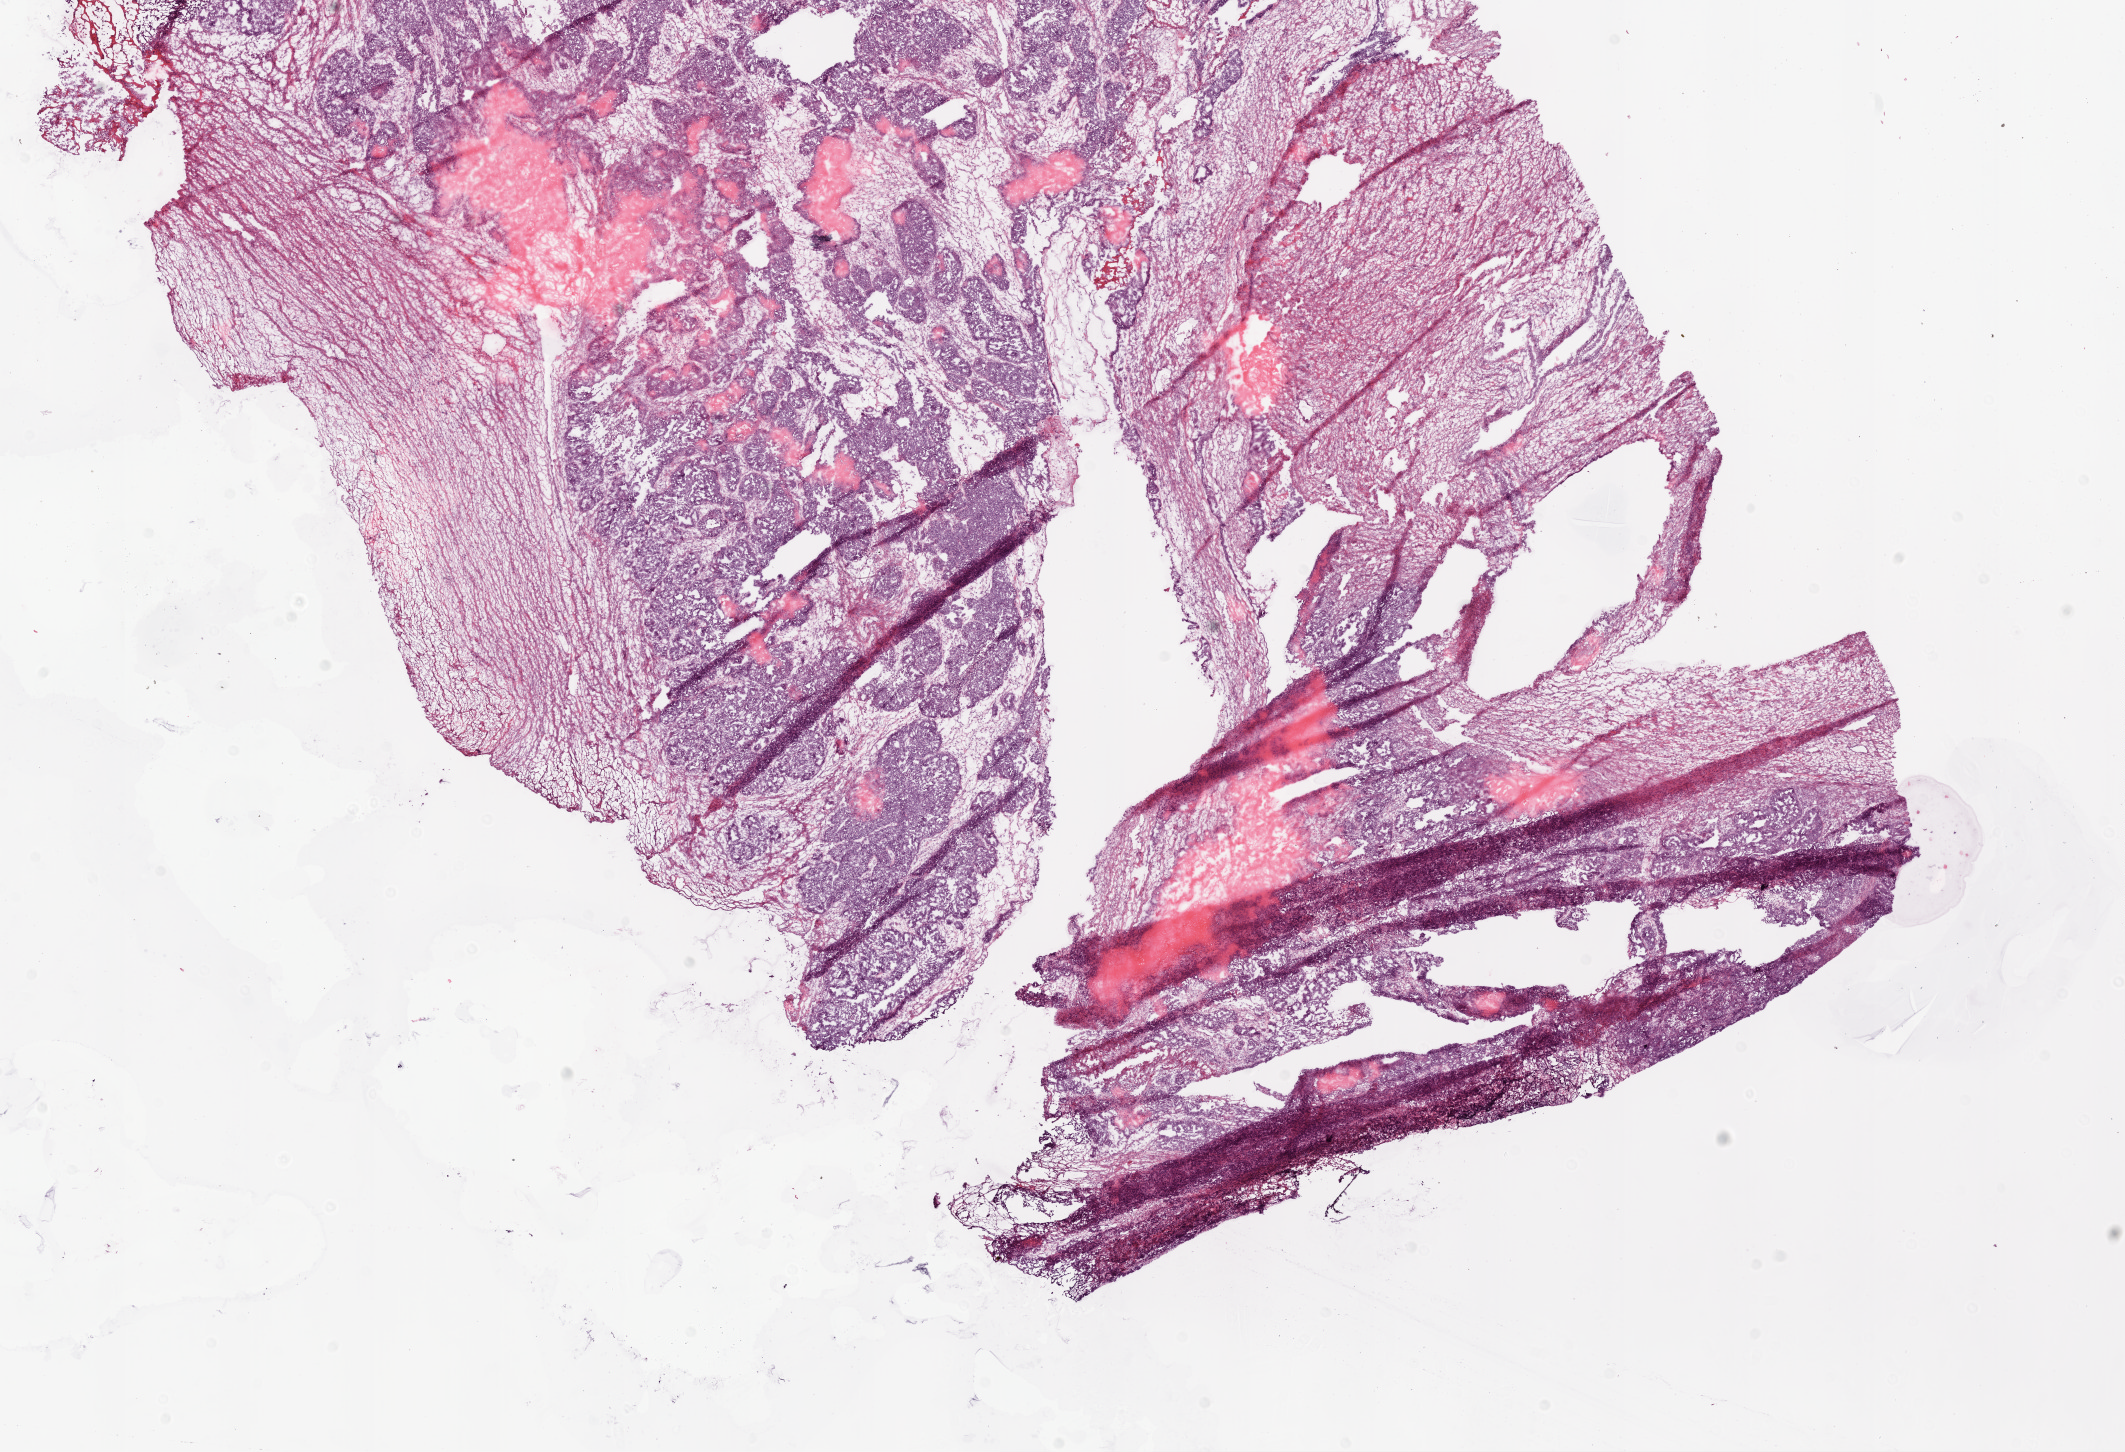
H&E-stained whole-slide image, a low-resolution overview of the entire scanned area, about 17.1 x 11.7 mm, frozen section, ovary, primary tumour sample. Patient: female, age at initial diagnosis 71 years. Histologic grade: G2 (moderately differentiated). Composition of this section per pathologist review: tumour cells 80%, tumour nuclei 80%, normal cells 0%, stromal cells 20%, necrosis 0%. Infiltration values recorded for this section: lymphocyte infiltration 0%, monocyte infiltration 0%, neutrophil infiltration 0%.
• laterality: bilateral
• histologic diagnosis: Serous cystadenocarcinoma, NOS
• FIGO stage: IIC